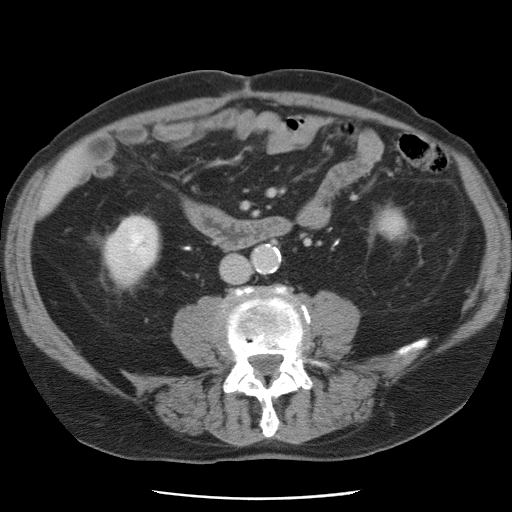
Contrast-enhanced abdominal CT, one axial slice; slice 11 of 78 in the series (ordered by position); 120 kVp; soft-tissue window (W 400 / L 40 HU); 5 mm slice thickness; 512 × 512 image matrix. Male patient, age 75 years. From the clinical record (not read from this slice): diagnosis: colorectal cancer liver metastases, imaged before liver resection; multiple liver metastases: yes.
Annotated regions visible in this slice (manually delineated by an expert):
- liver: bounding box [x1, y1, x2, y2] px = [43, 154, 81, 210]
- planned liver remnant (the part of the liver to remain after resection): [43, 155, 81, 210]